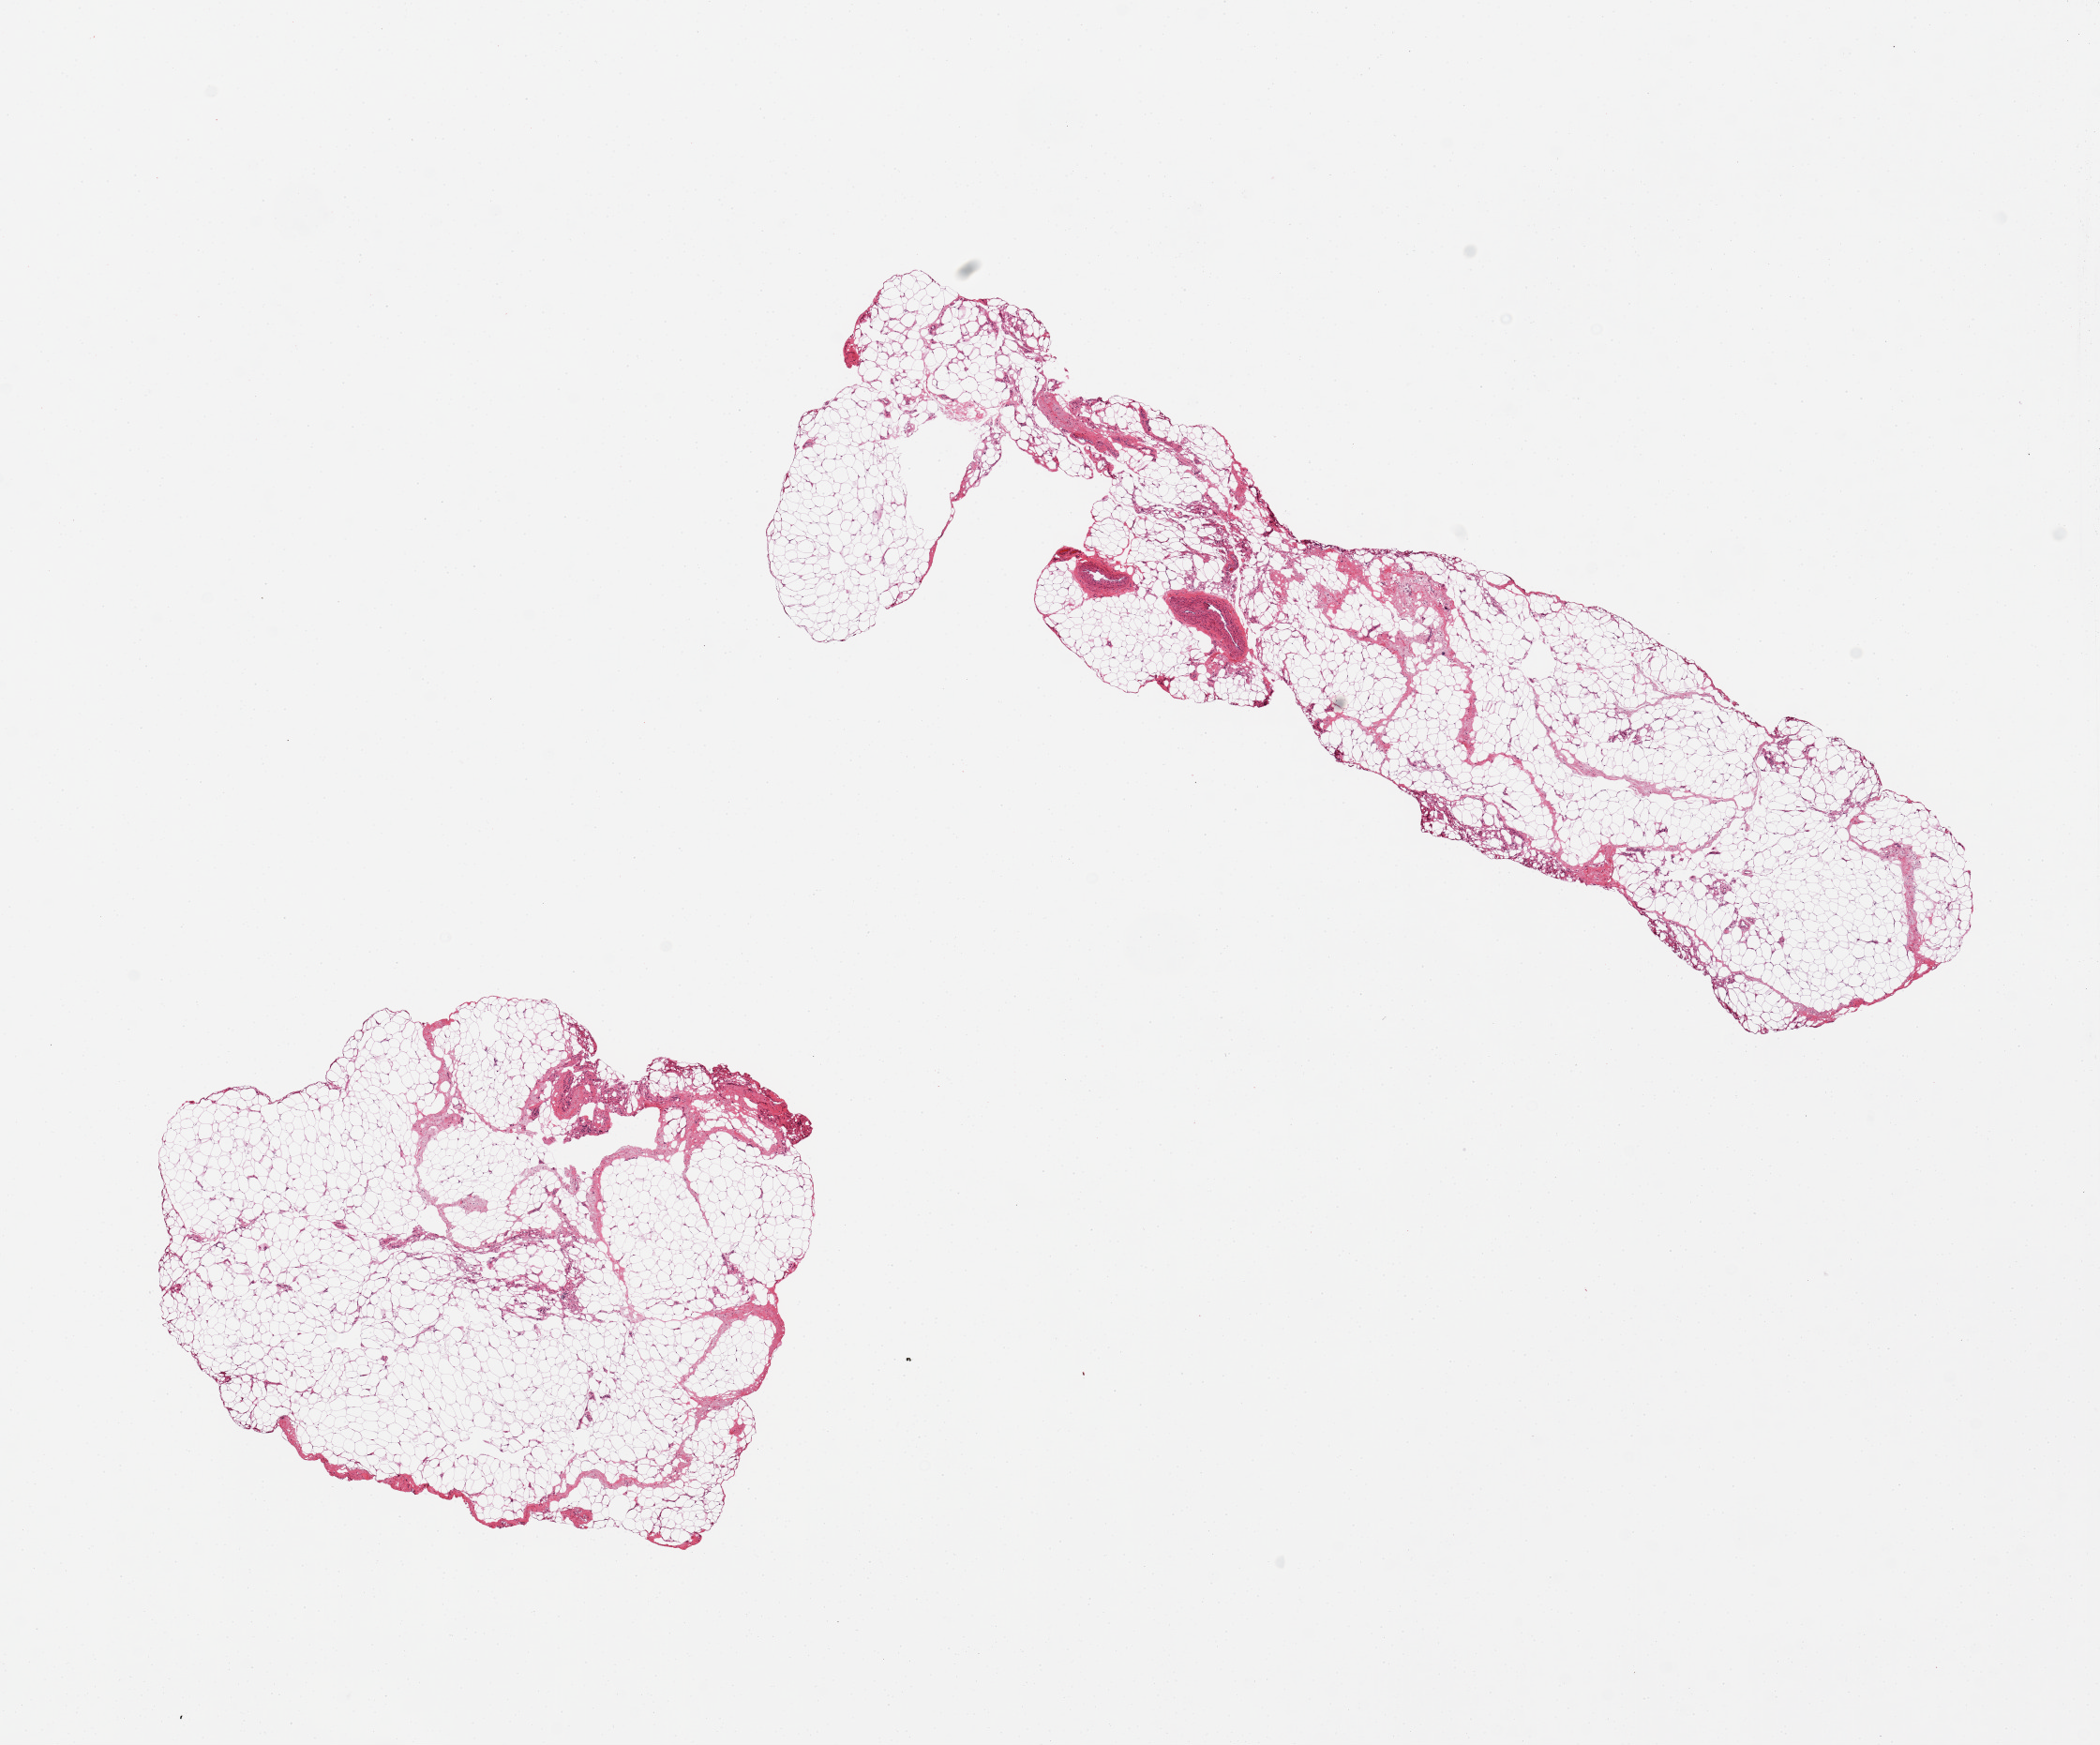
Haematoxylin and eosin whole-slide image — a low-resolution overview of the entire scanned area, about 17.7 x 14.7 mm. PAXgene-fixed paraffin-embedded (PFPE) section. Target tissue: adipose tissue. Donor tissue sample. Donor sex: female.
* reviewer comment on this tissue sample: 2 pieces